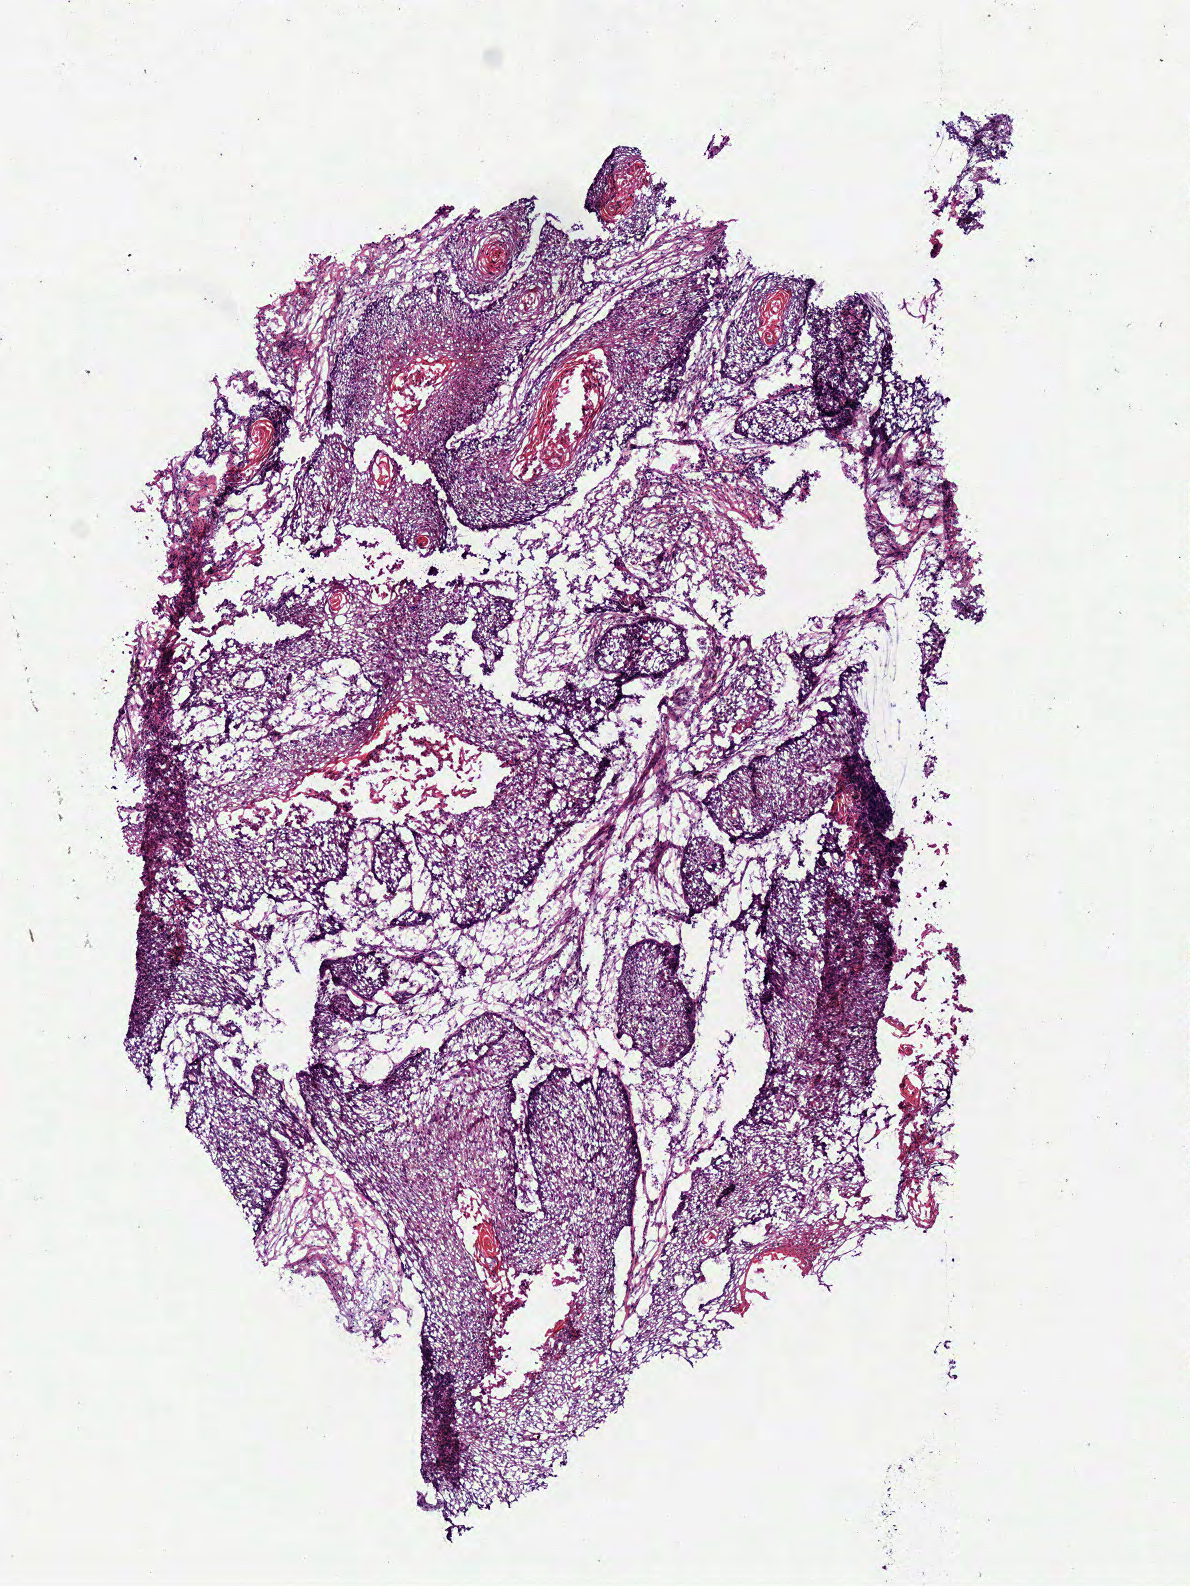
Whole-slide histology image, H&E-stained — shown as a low-resolution overview of the whole scanned area (about 4.7 x 6.2 mm, slide scanned at 40x); frozen section from the bottom of the tissue portion; sample: primary tumour, head and neck. Female patient; age at initial diagnosis 53 years. Histologic grade: G2 (moderately differentiated). Slide review estimates, as recorded: tumour cells 80%, tumour nuclei 80%, normal cells 0%, stromal cells 20%, necrosis 0%.
TNM: T4a N3. AJCC pathologic stage: IVB (7th edition). Histologic diagnosis: Squamous cell carcinoma, NOS.